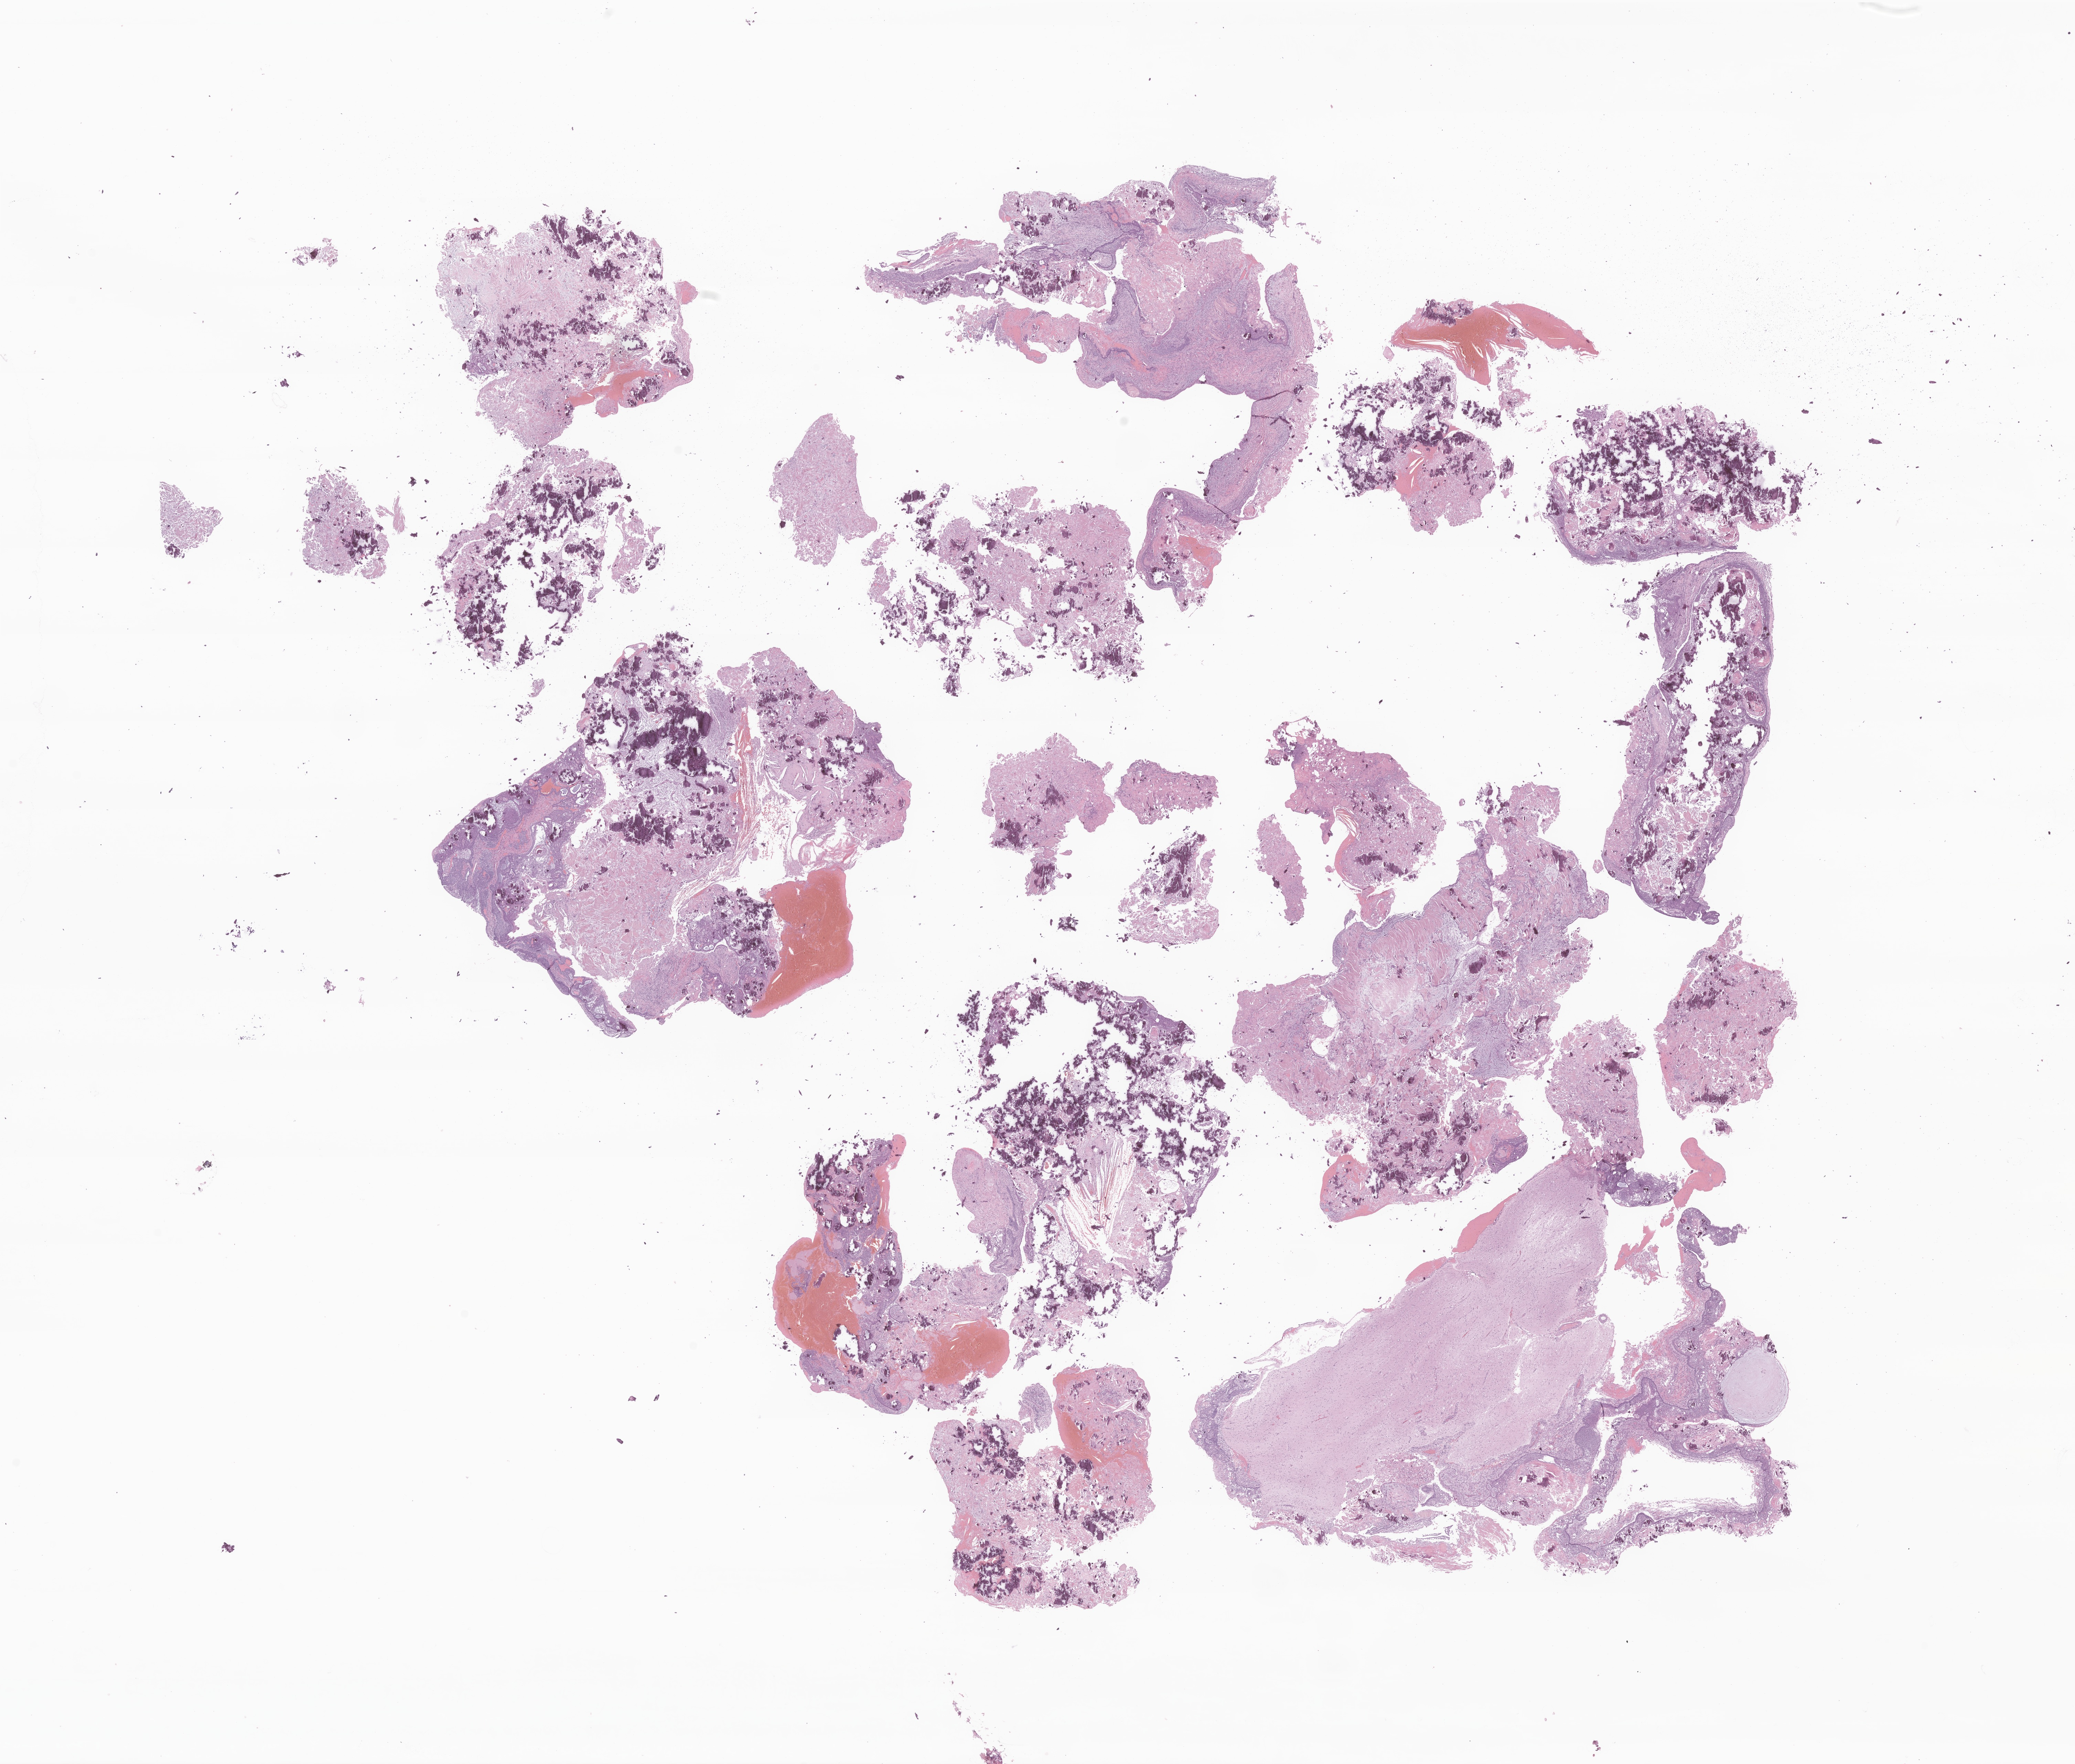
Digitized haematoxylin and eosin-stained section of tumor tissue from the brain, whole scanned area (about 25.4 x 21.6 mm) shown as a low-resolution overview, formalin-fixed, paraffin-embedded (FFPE) tissue. Female patient, age 86 months (7 years 2 months).
Diagnosis: Craniopharyngioma, adamantinomatous.